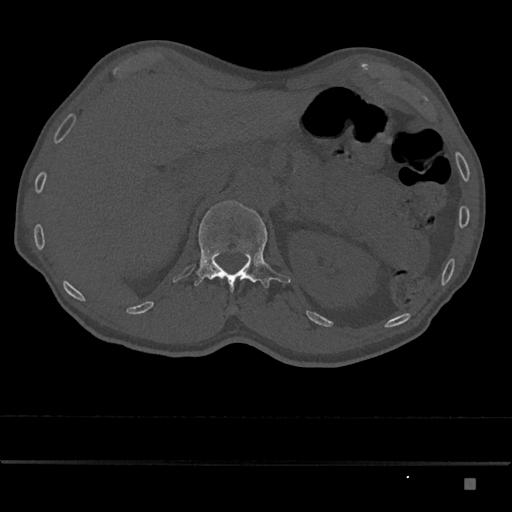
CT including the spine, one axial slice; slice 550 of 797 in the series (ordered by position); 120 kVp; bone window (W 1800 / L 400 HU); 512 × 512 image matrix, field of view 390 × 390 mm. Patient: male, 72 years. Case-level facts recorded for this patient, not image findings: primary cancer: prostate.
Annotated regions visible in this slice (semi-automatic segmentation, software-assisted and operator-edited):
- L1 vertebra: box from (x=194, y=200) to (x=291, y=293) px